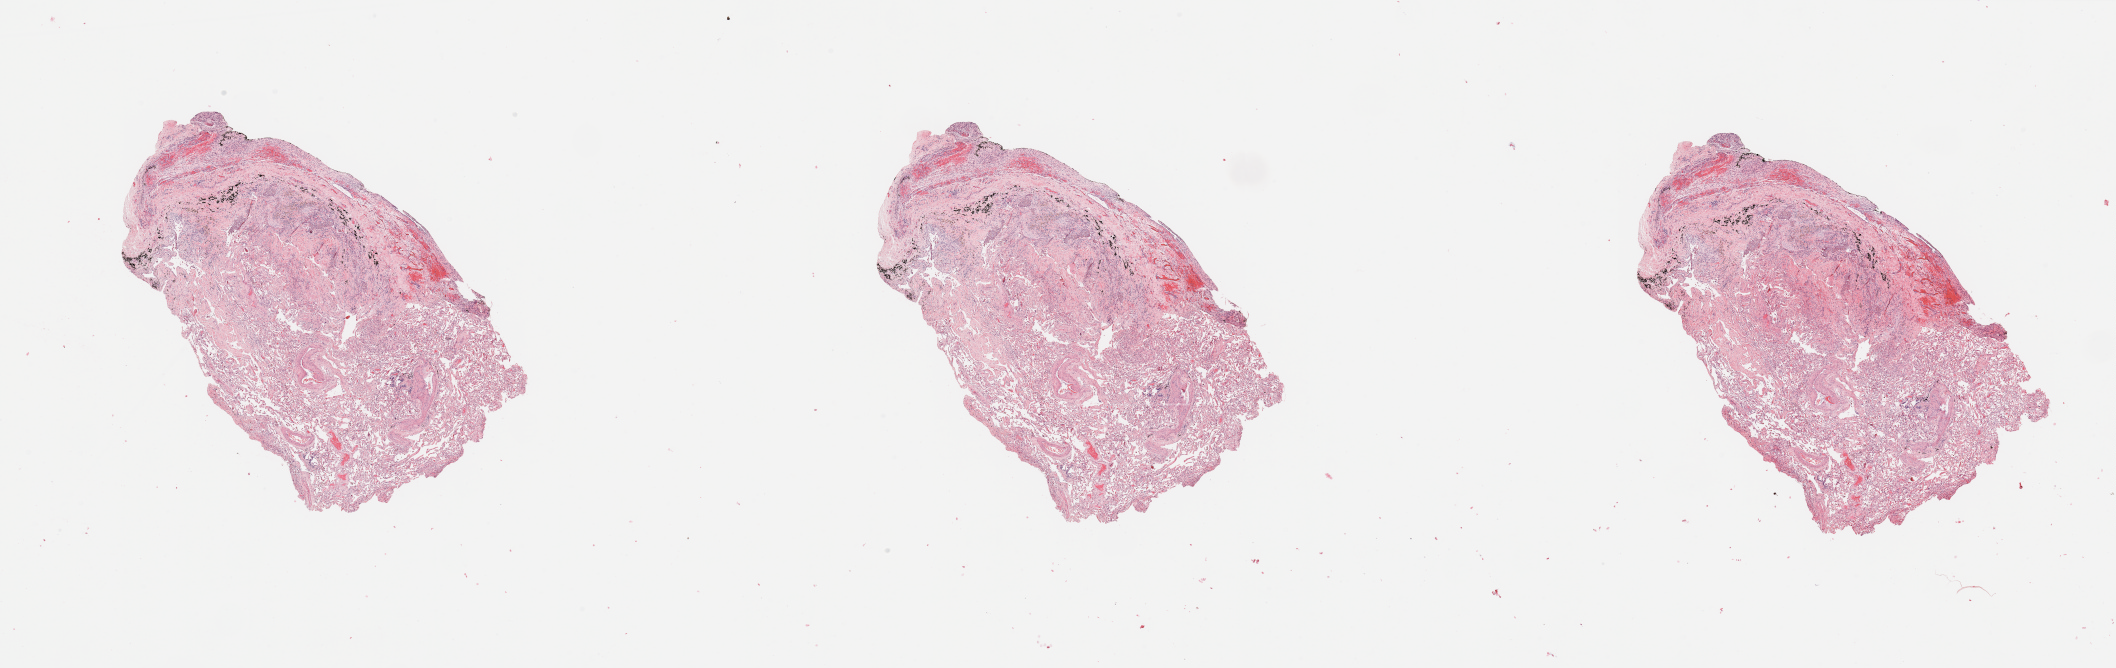
Whole-slide histology image, H&E-stained — whole scanned area (about 33.5 x 10.6 mm) shown as a low-resolution overview. Normal (non-tumour) tissue sample, sampled site: lung. 70-year-old female patient.
- this section: normal (non-tumour) tissue from the same patient
- patient diagnosis: Adenocarcinoma, NOS